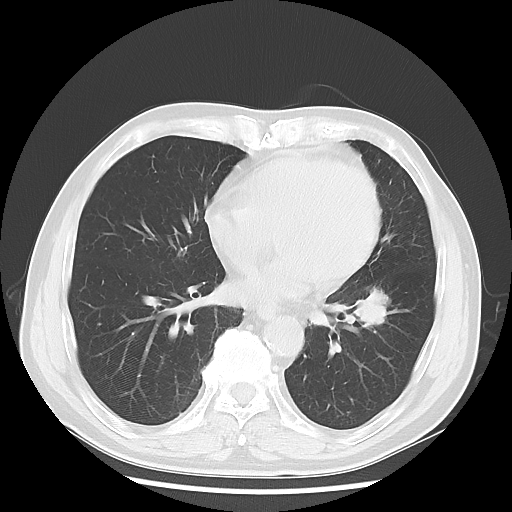
Chest CT, one axial slice. Position 27 of 68 along the scan axis. Lung window (W 1500 / L -600 HU). 5 mm slice thickness. 512 × 512 image matrix. Patient: male, 71 years. From the clinical record (not read from this slice): clinical TNM (as recorded): T1c N1 M0; histopathological grade: G2-3.
Outlined on this slice (rectangle marked by the reading radiologist):
- lung tumour (recorded histology: adenocarcinoma): bounding box (x1, y1, x2, y2) in pixels: (349, 277, 394, 340)